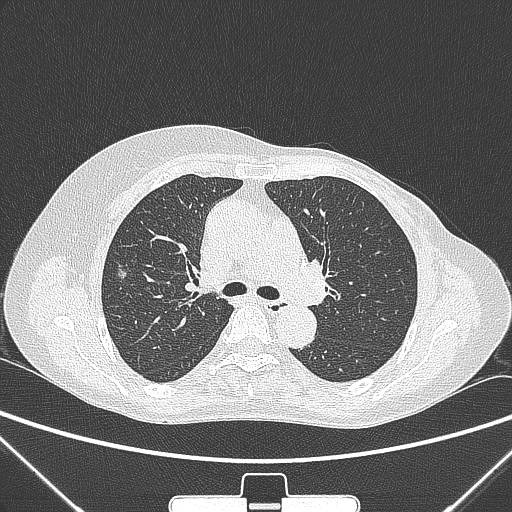
Chest CT, one axial slice. Position 163 of 265 along the scan axis. 120 kVp. Lung window (W 1500 / L -600 HU). 512 × 512 image matrix, field of view 350 × 350 mm. Female patient, age 64 years. From the clinical record (not read from this slice): clinical TNM (as recorded): T1c N0 M0; histopathological grade: G1-2.
Outlined on this slice (rectangle marked by the reading radiologist):
- lung tumour (recorded histology: adenocarcinoma): box from (x=108, y=260) to (x=133, y=286) px